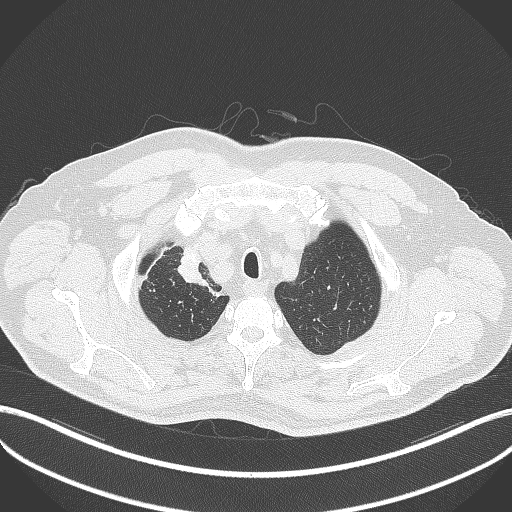
Chest CT, one axial slice. Slice 337 of 411 in the series (ordered by position). Reconstruction kernel B70f. 120 kVp. Lung window (W 1500 / L -600 HU). 1 mm slice thickness. 512 × 512 image matrix, field of view 400 × 400 mm. Patient: male, 60 years. Case-level facts recorded for this patient, not image findings: clinical TNM (as recorded): T1b N1 M0.
Structures marked on this image (rectangle marked by the reading radiologist):
- lung tumour (recorded histology: squamous cell carcinoma): bounding box <175,246,205,286> (left, top, right, bottom; pixels)